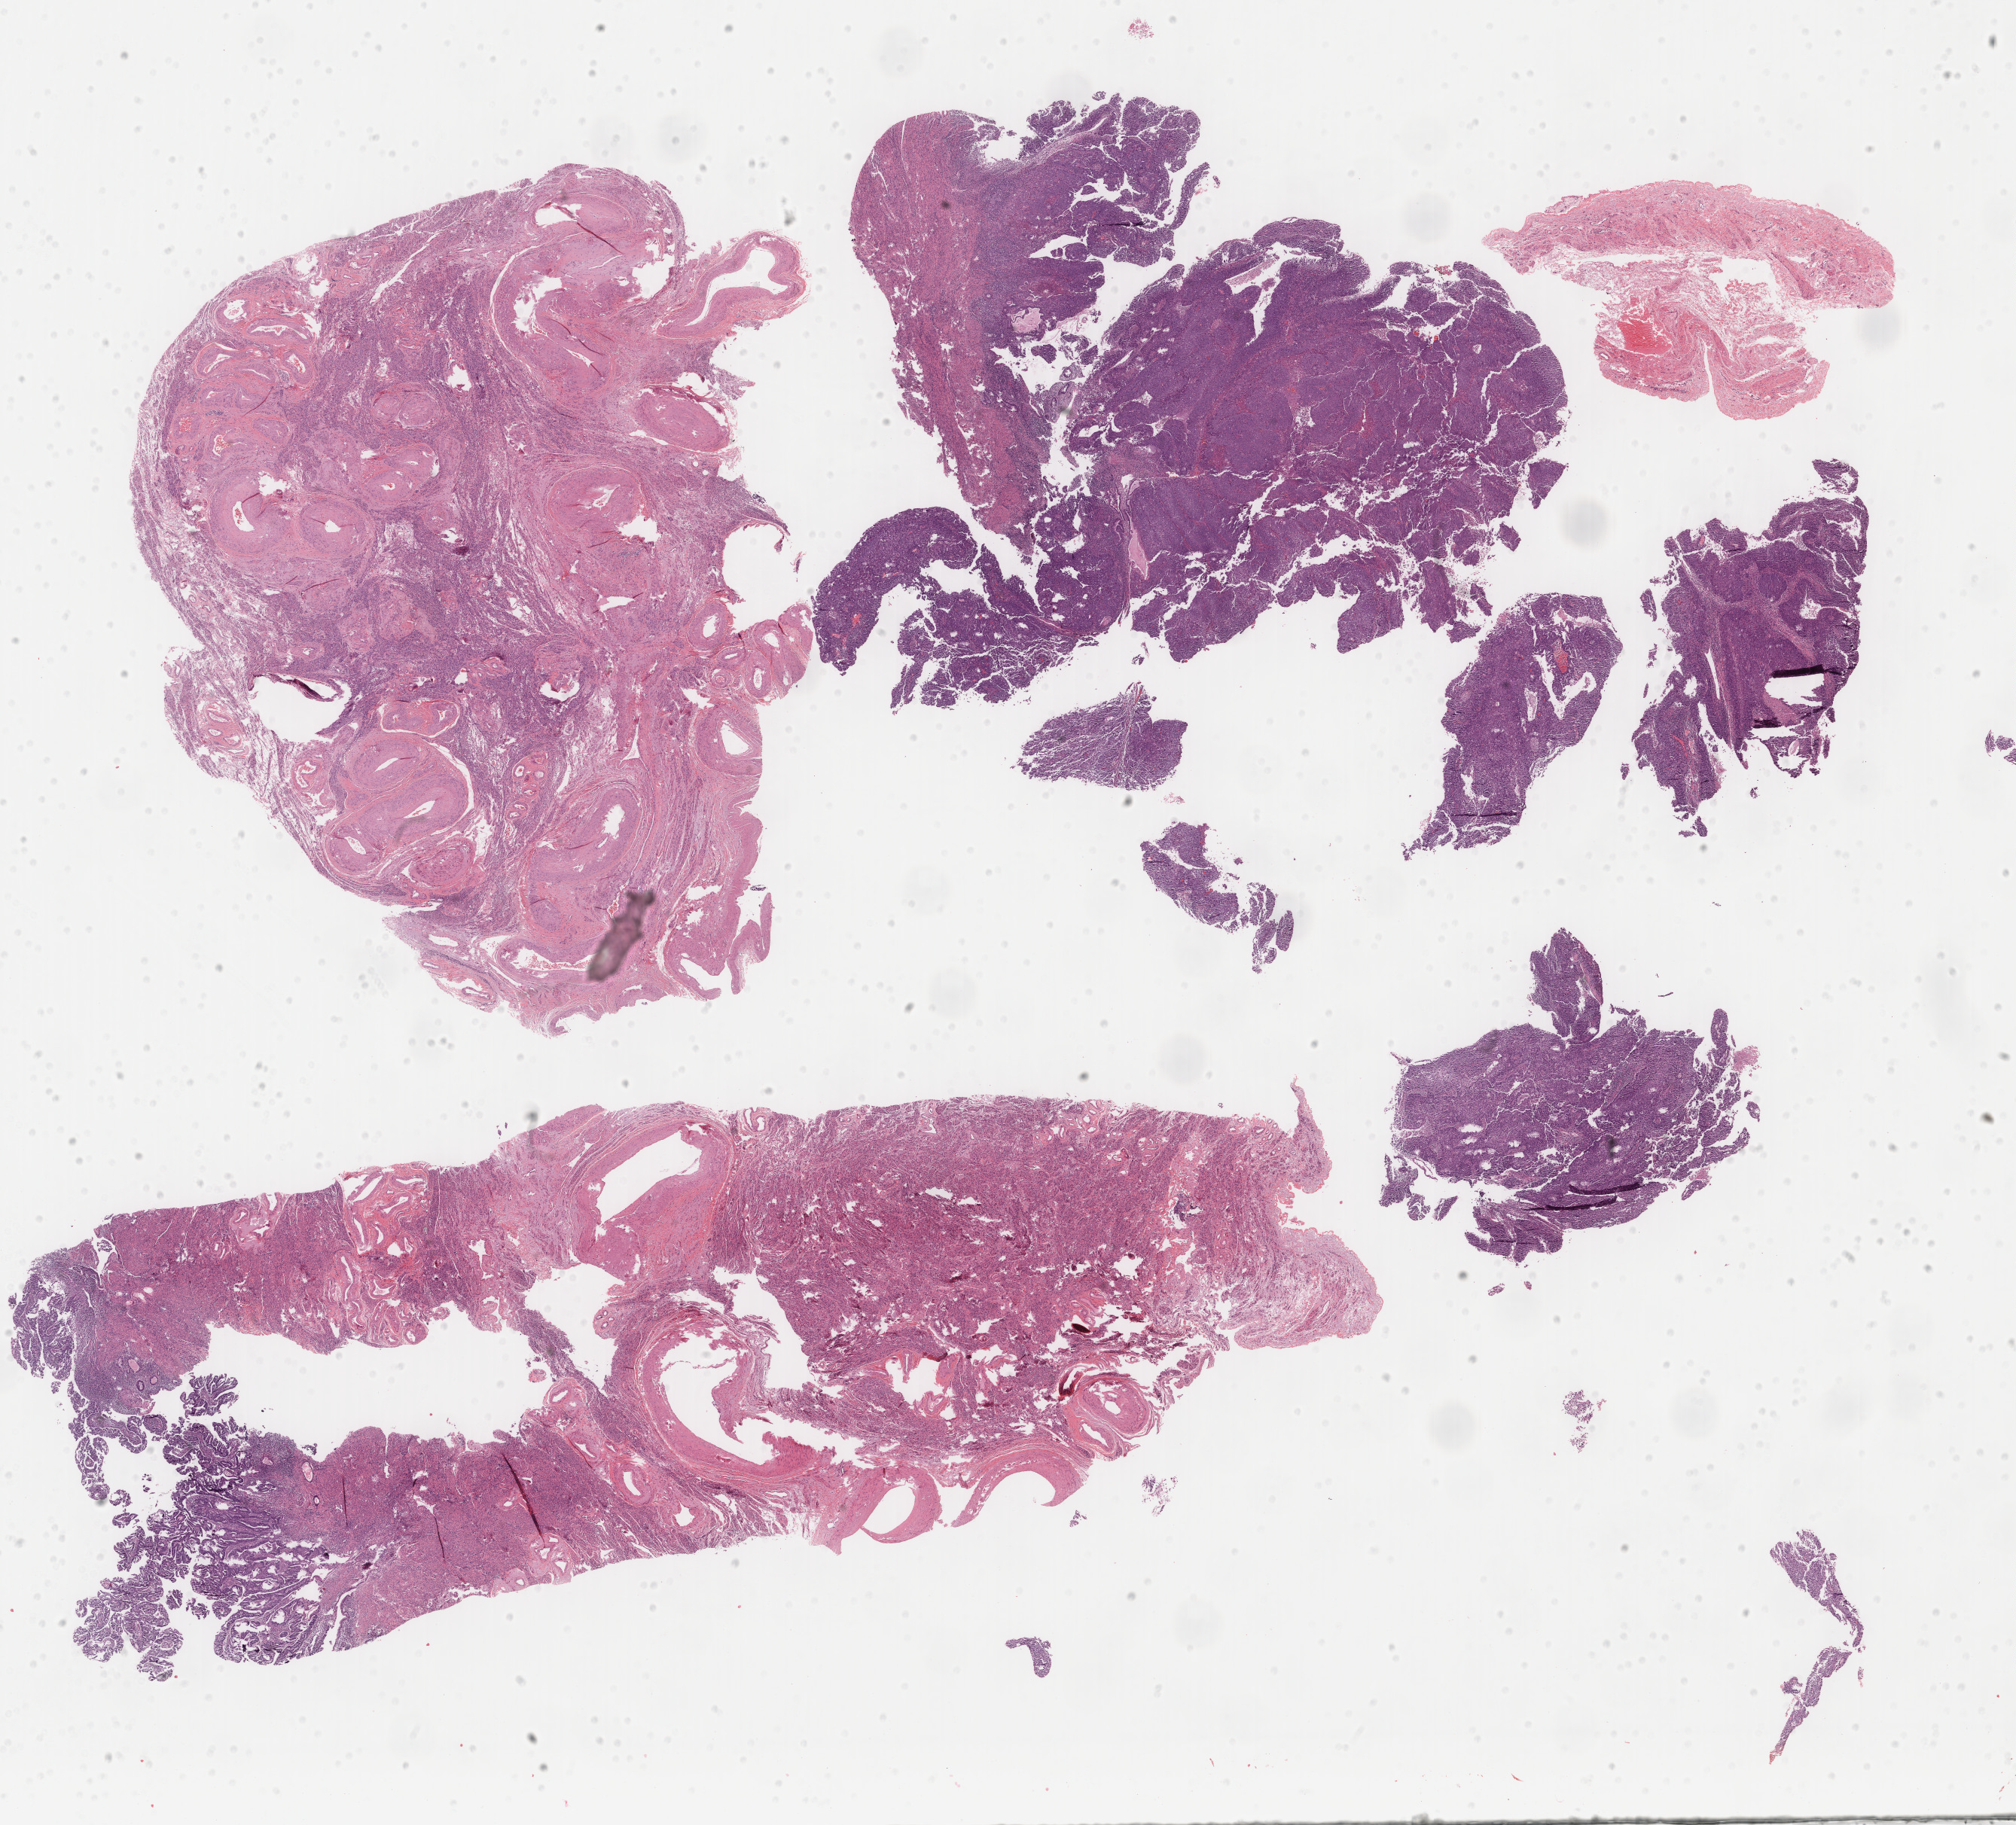
Digitized H&E-stained tissue section (whole slide) — a low-resolution overview of the entire scanned area, about 21.2 x 19.2 mm (slide scanned at 40x). FFPE section. Uterus, primary tumour sample. Patient: female, age at initial diagnosis 70 years.
Histologic diagnosis: Serous cystadenocarcinoma, NOS (endometrium).